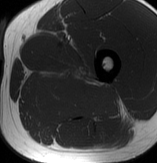
MRI of an extremity soft-tissue mass, one axial slice; slice 48 of 70 in the series (ordered by position); MR volume resampled by the dataset authors to the PET/CT grid (not the native acquisition matrix); 157 × 163 image matrix. Male patient. Case-level facts recorded for this patient, not image findings: histological type: extraskeletal osteosarcoma; grade: high; site of the primary tumour: left adductur.
Structures marked on this image (expert contour drawn on MRI and transferred to this co-registered scan by the dataset authors):
- gross tumour volume (mass): bounding box <31,63,121,123> (left, top, right, bottom; pixels)